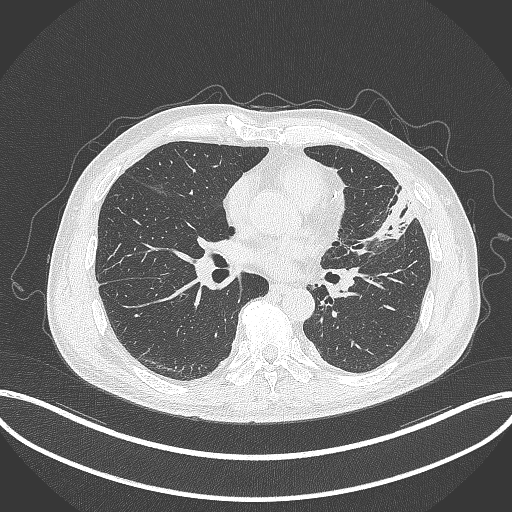
Chest CT, one axial slice. Position 159 of 382 along the scan axis. 120 kVp. Lung window (W 1500 / L -600 HU). 1 mm slice thickness. 512 × 512 image matrix, field of view 415 × 415 mm. Male patient, age 64 years. From the clinical record (not read from this slice): clinical TNM (as recorded): T4 N1 M0; histopathological grade: G3.
Annotated regions visible in this slice (bounding box drawn by a radiologist):
- lung tumour (recorded histology: adenocarcinoma): bounding box <365,186,417,244> (left, top, right, bottom; pixels)